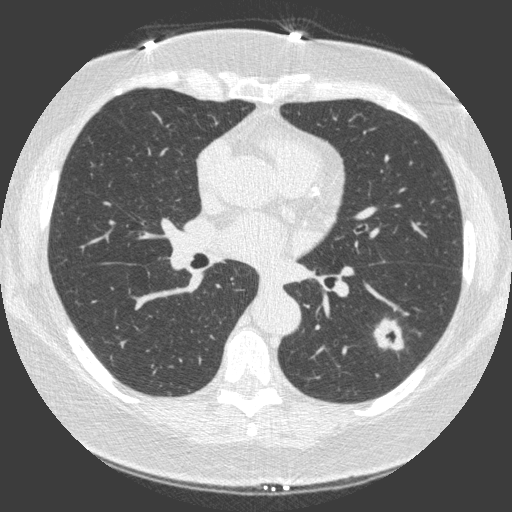
Low-dose screening chest CT, one axial slice; position 85 of 149 along the scan axis; 120 kVp; lung window (W 1500 / L -600 HU); 1 mm slice thickness; 512 × 512 image matrix, field of view 330 × 330 mm.
Annotated regions visible in this slice (expert manual segmentation):
- lesion 1 (tumor, lower lobe of left lung): bounding box (x1, y1, x2, y2) in pixels: (374, 319, 404, 351)